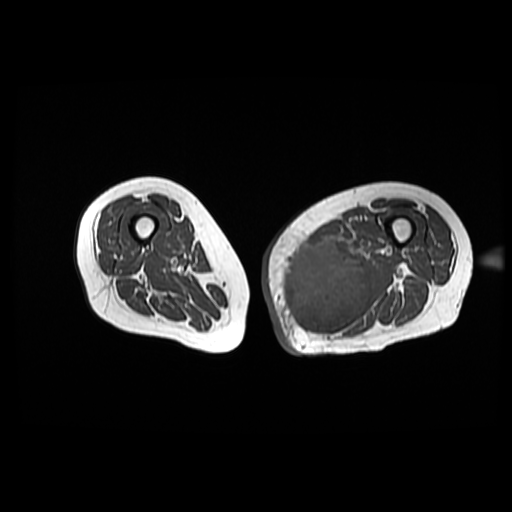
MRI of an extremity soft-tissue mass, one axial slice. Position 33 of 42 along the scan axis. 512 × 512 image matrix. Female patient. Case-level facts recorded for this patient, not image findings: histological type: pleomorphic leiomyosarcoma; grade: high; site of the primary tumour: left thigh.
Annotated regions visible in this slice (expert manual segmentation):
- gross tumour volume including surrounding oedema: bounding box [x1, y1, x2, y2] px = [279, 239, 381, 338]
- gross tumour volume (mass): [279, 241, 373, 338]